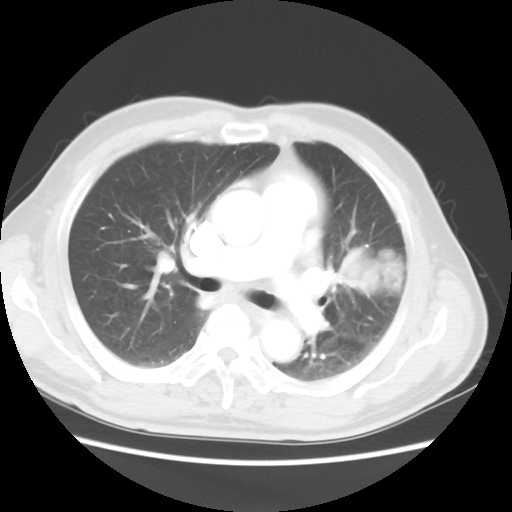
Chest CT, one axial slice; position 30 of 50 along the scan axis; reconstruction kernel STANDARD; 120 kVp; lung window (W 1500 / L -600 HU); 512 × 512 image matrix. Male patient, age 69 years. Case-level facts recorded for this patient, not image findings: clinical TNM (as recorded): T3 N1 M1a.
Annotated regions visible in this slice (bounding box drawn by a radiologist):
- lung tumour (recorded histology: squamous cell carcinoma): bounding box <330,241,408,300> (left, top, right, bottom; pixels)